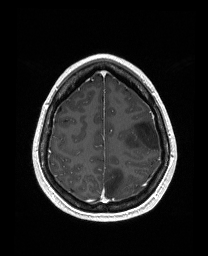
Brain MRI from a brain-tumour surgery series, one axial slice; position 125 of 176 along the scan axis; T1-weighted post-contrast; 208 × 256 image matrix, field of view 203 × 250 mm. Case-level facts recorded for this patient, not image findings: histopathology: Astrocytoma; WHO grade: 3; IDH mutation: yes; tumour location: Left Frontal.
Annotated regions visible in this slice (outlined manually by an expert reader):
- tumour: bounding box <124,118,159,151> (left, top, right, bottom; pixels)